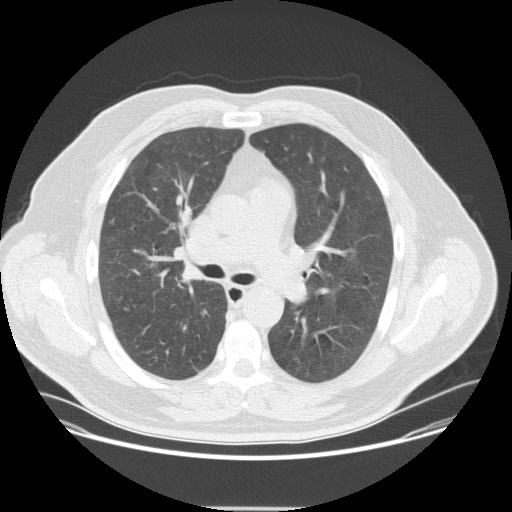
Low-dose screening chest CT, one axial slice. 120 kVp. Lung window (W 1500 / L -600 HU). 2.5 mm slice thickness. 512 × 512 image matrix, field of view 419 × 419 mm.
Annotated regions visible in this slice (manually delineated by an expert):
- lesion 1 (tumor, upper lobe of right lung): bounding box [x1, y1, x2, y2] px = [181, 272, 197, 284]